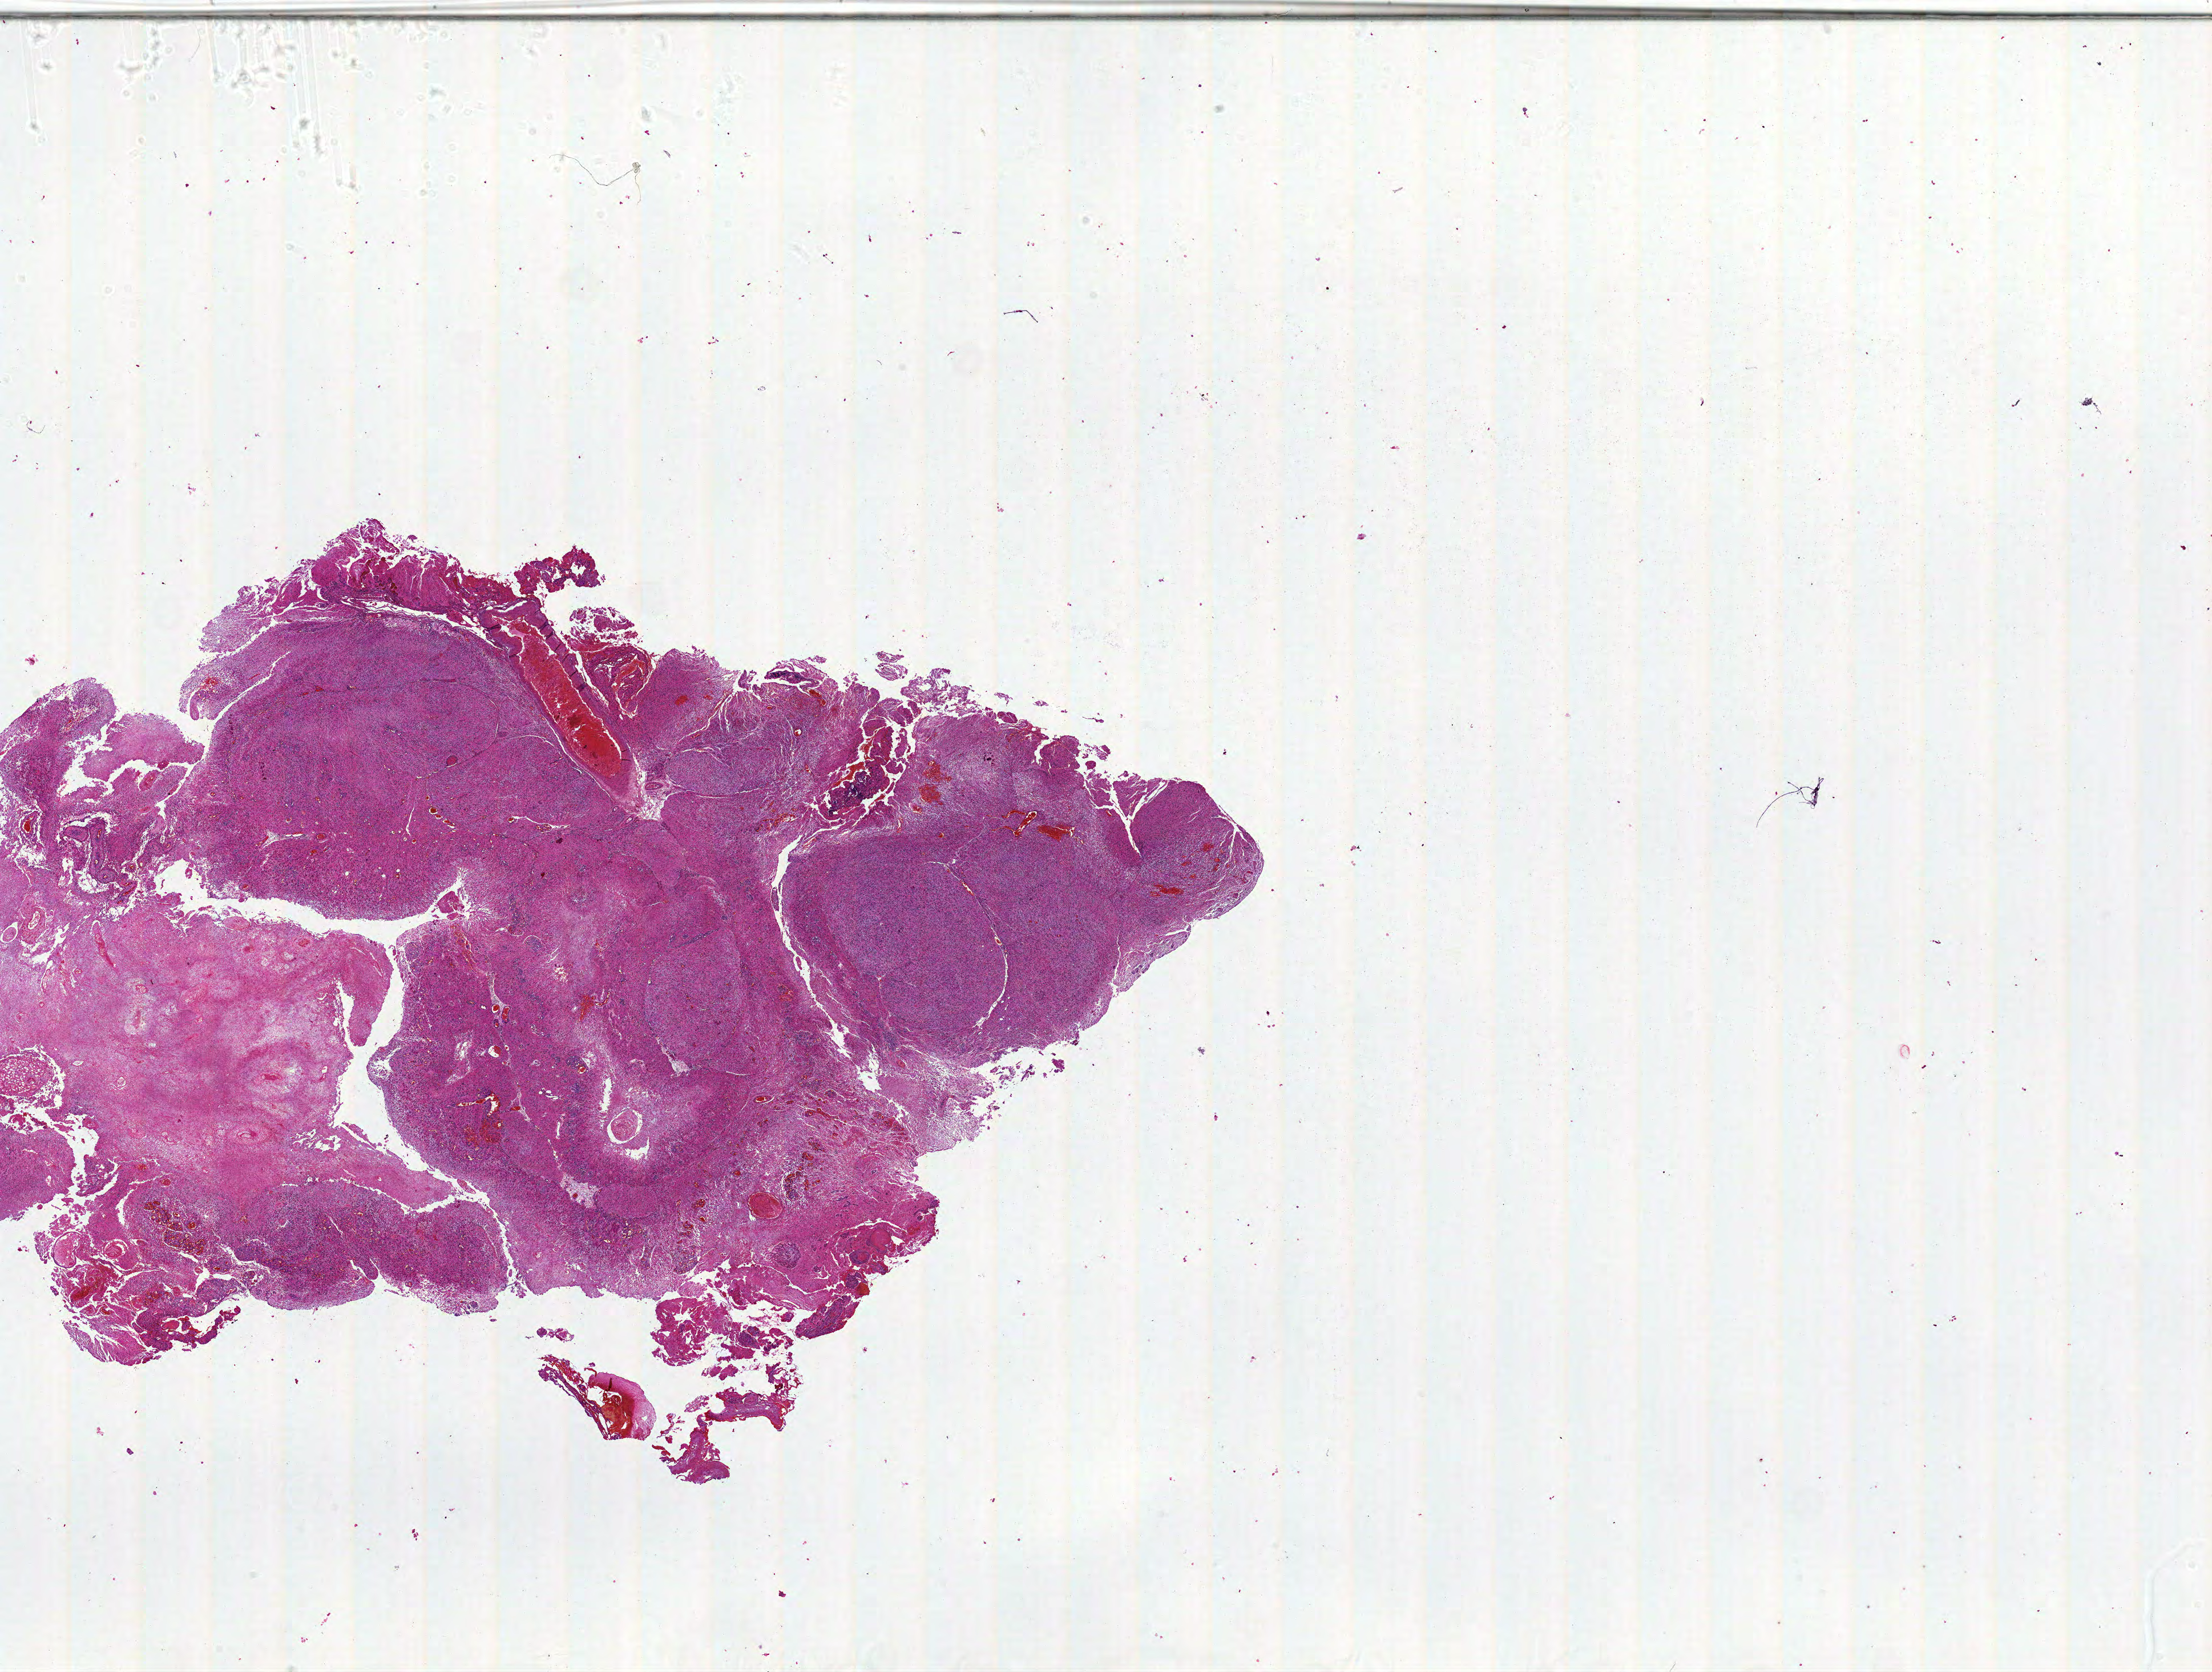
Whole-slide histology image, Hematoxylin and eosin (H&E) stained, a low-resolution overview of the entire scanned area, about 31.0 x 23.4 mm; formalin-fixed paraffin-embedded (FFPE) diagnostic section; sample: primary tumour, brain. Male patient; age at initial diagnosis 57 years.
Diagnosis: Glioblastoma.